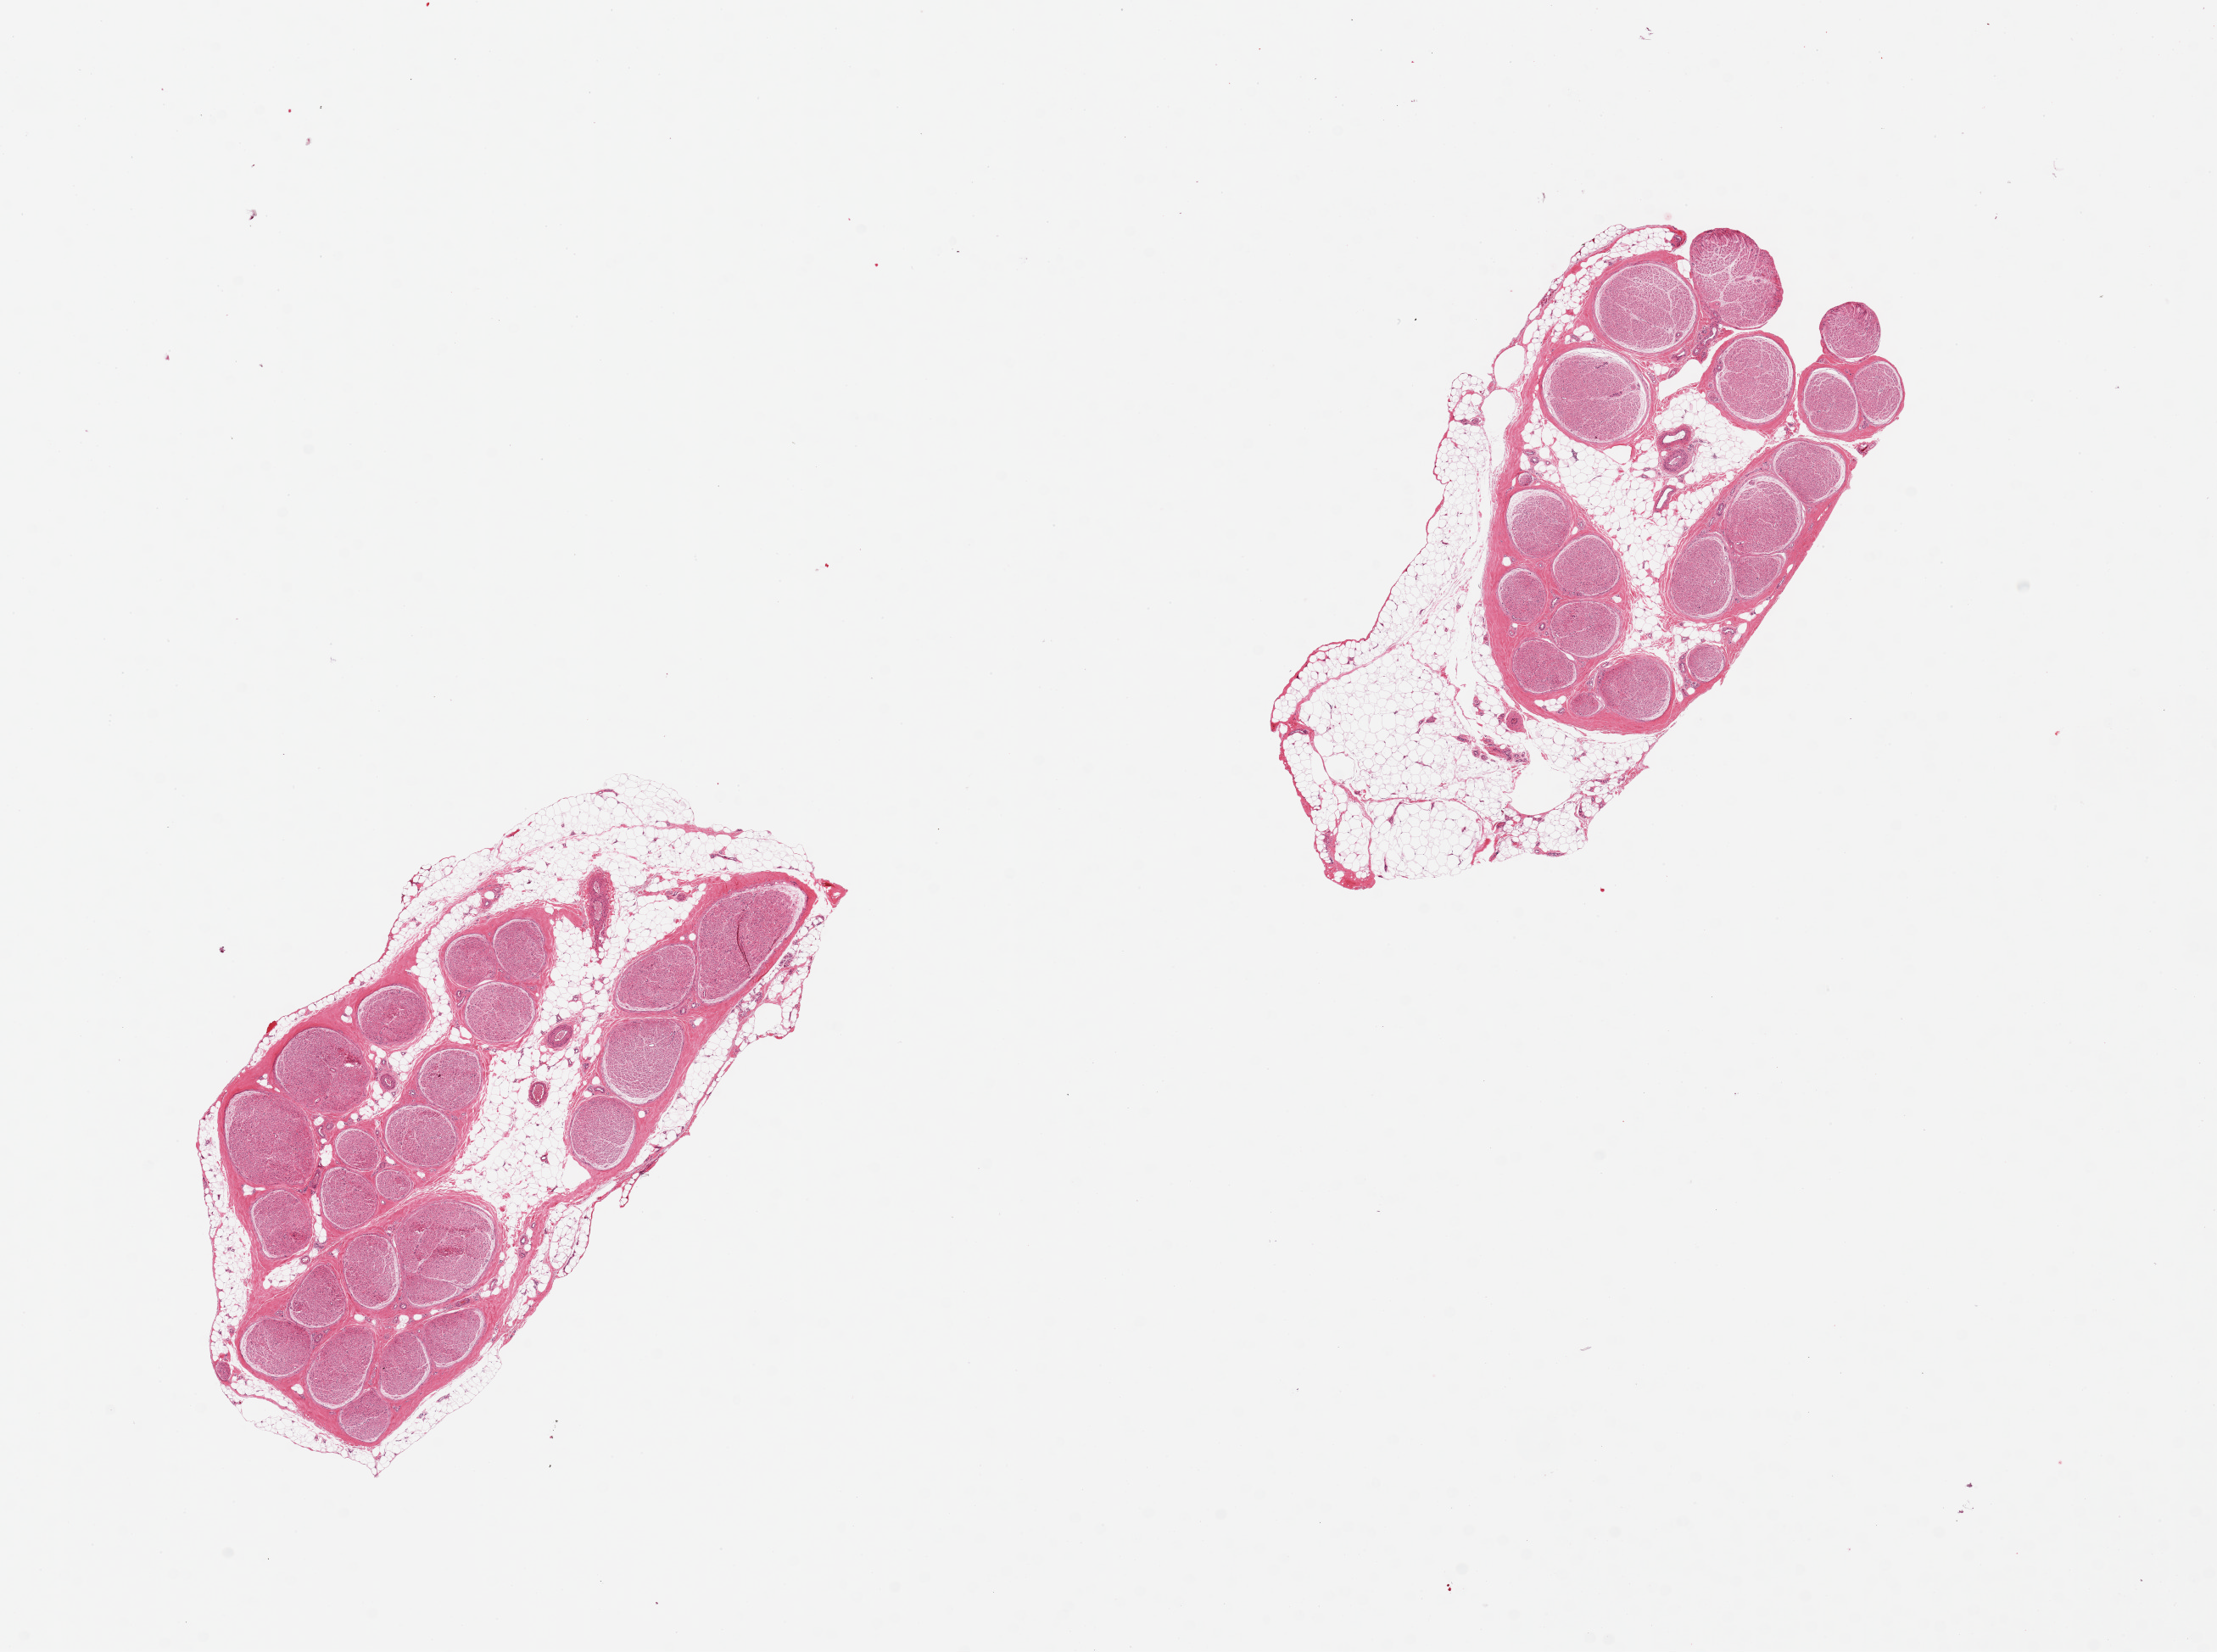
Whole-slide image, hematoxylin and eosin (H&E) stain, brightfield, low-resolution overview of the scanned area, about 20.7 x 15.4 mm (slide scanned at 20x). PAXgene-fixed paraffin-embedded (PFPE) section. Sampled site (target tissue): tibial nerve. Tissue donor sample.
Review note (as recorded): 2 pieces; 1 with 40% external and 10% internal fat; other with 20% internal and 20% external fat.